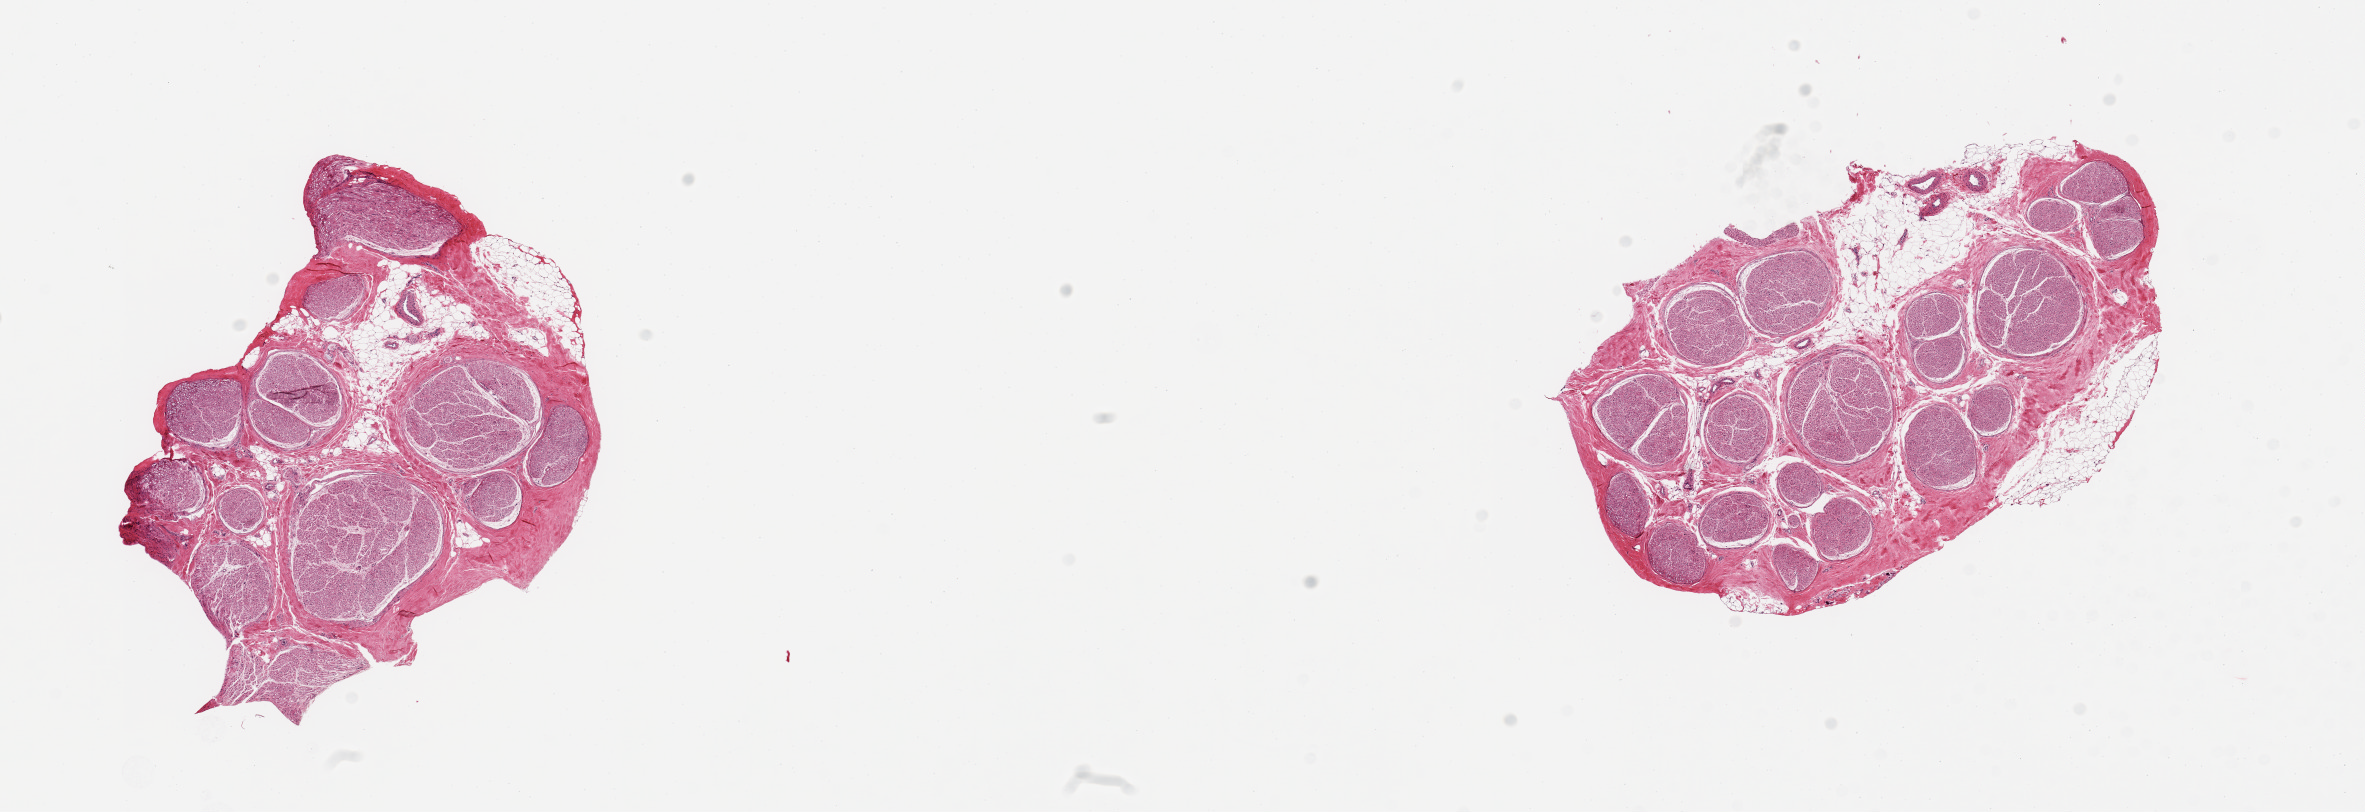
Whole-slide image, haematoxylin and eosin stain — a low-resolution overview of the entire scanned area, about 18.7 x 6.4 mm, PAXgene-fixed, paraffin-embedded tissue, target tissue: tibial nerve, donor tissue sample. Male donor.
Review note (as recorded): 2 pieces; includes up to 10% internal/external fat.